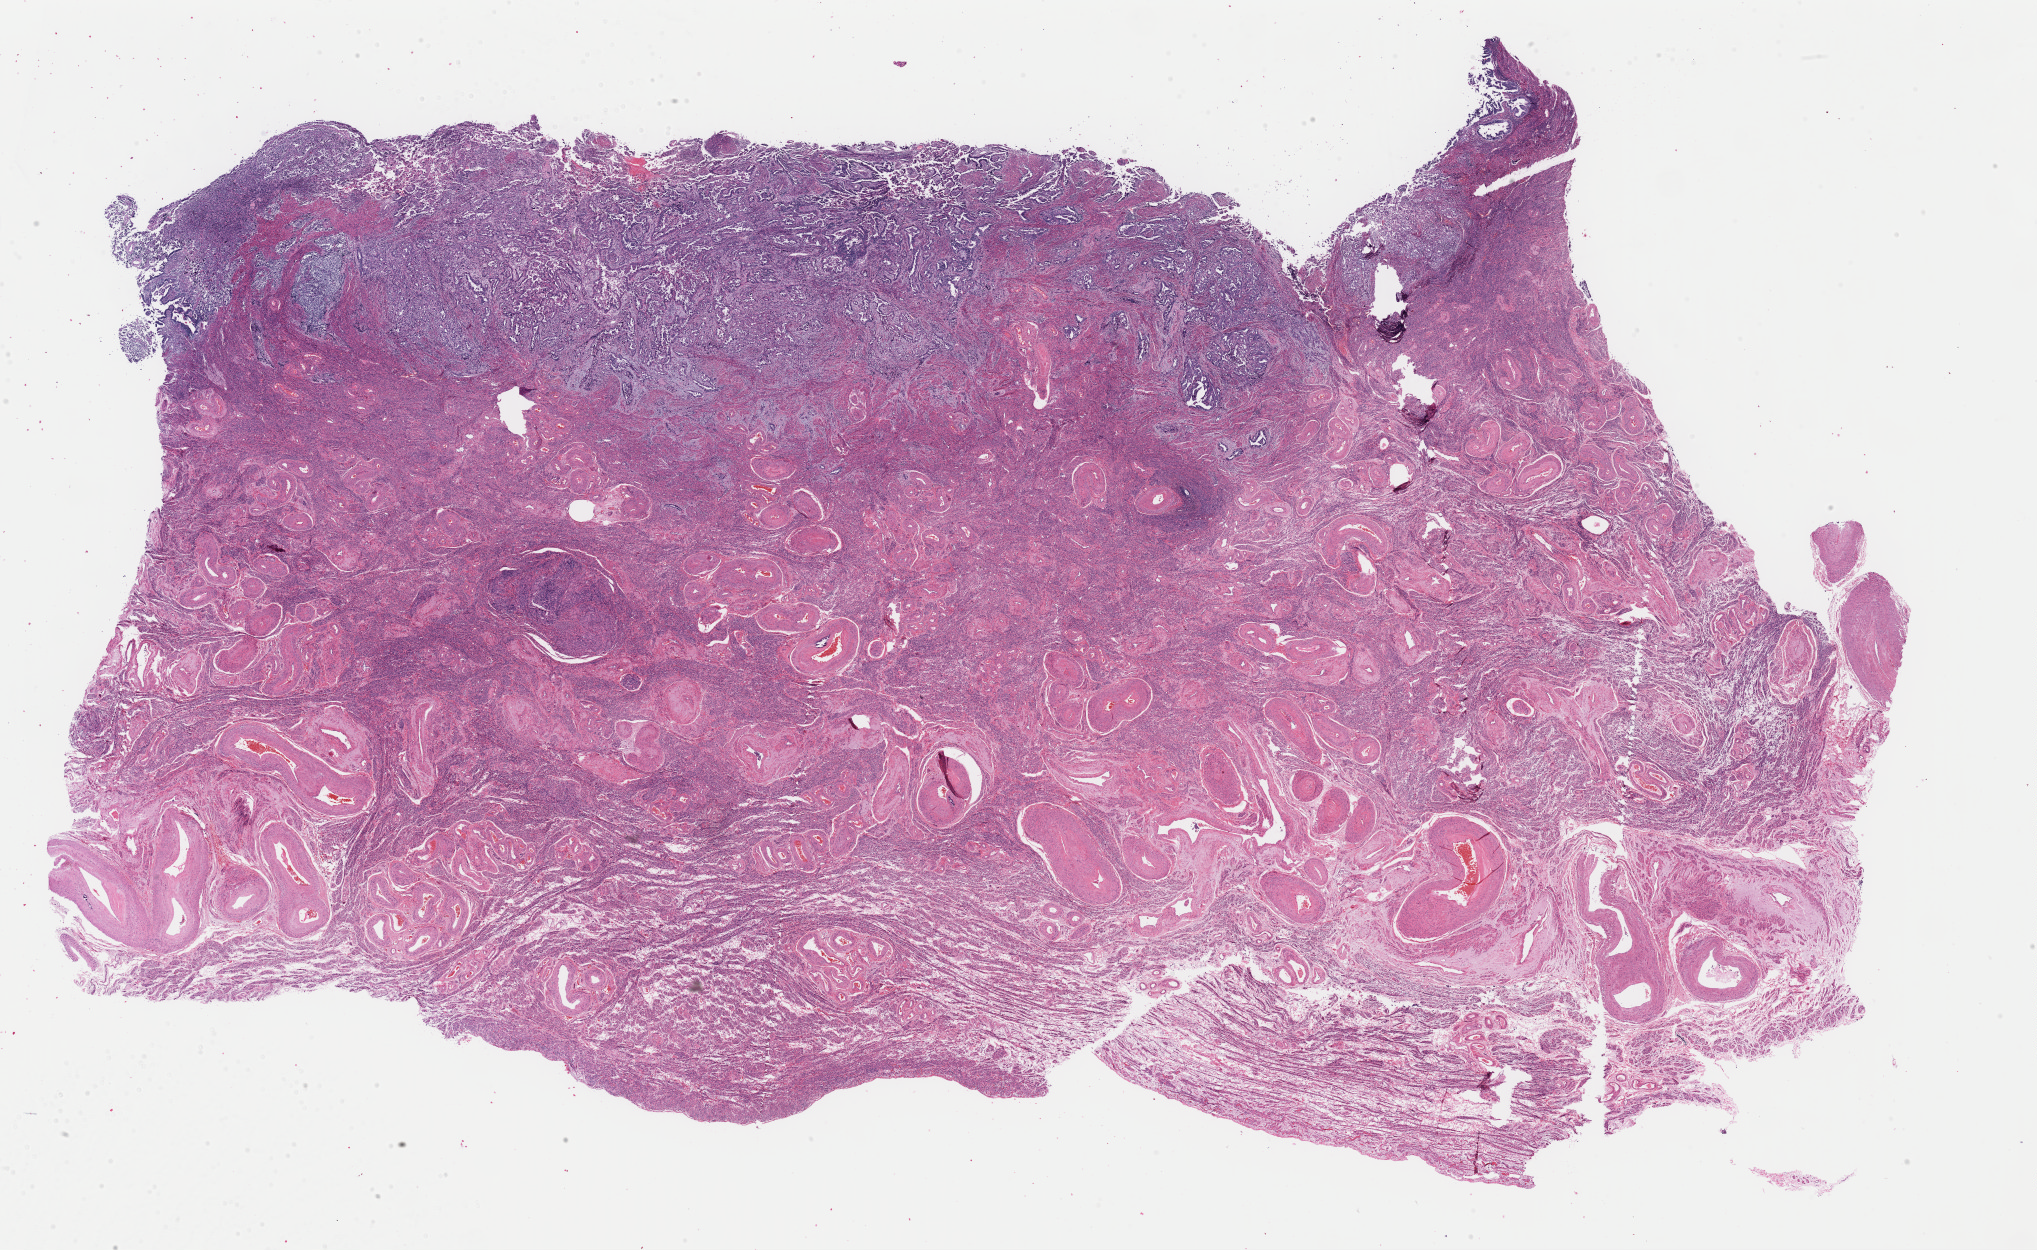
Digitized Hematoxylin and eosin (H&E) stained tissue section (whole slide) — low-resolution overview of the scanned area, about 32.2 x 19.8 mm (acquisition: 40x scan); FFPE section; sample: primary tumour, uterus. Female patient; age at initial diagnosis 80 years.
- FIGO stage: IVB
- histologic diagnosis: Carcinosarcoma, NOS (fundus uteri)